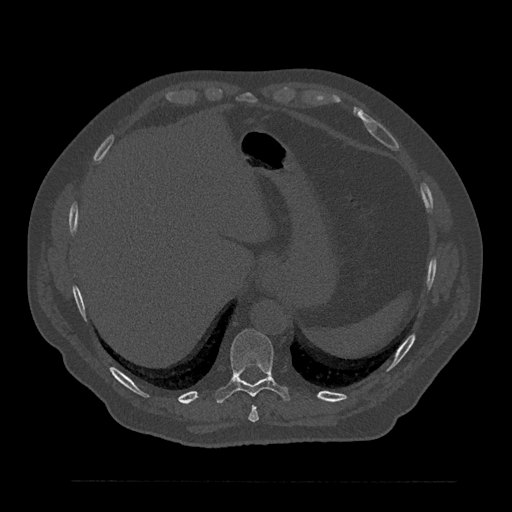
CT including the spine, one axial slice; 120 kVp; bone window (W 1800 / L 400 HU); 0.5 mm slice thickness; 512 × 512 image matrix. Male patient, age 61 years. From the clinical record (not read from this slice): primary cancer: prostate.
Outlined on this slice (semi-automatic segmentation, software-assisted and operator-edited):
- T10 vertebra: bounding box [x1, y1, x2, y2] px = [215, 329, 290, 403]
- T9 vertebra: [248, 406, 259, 422]